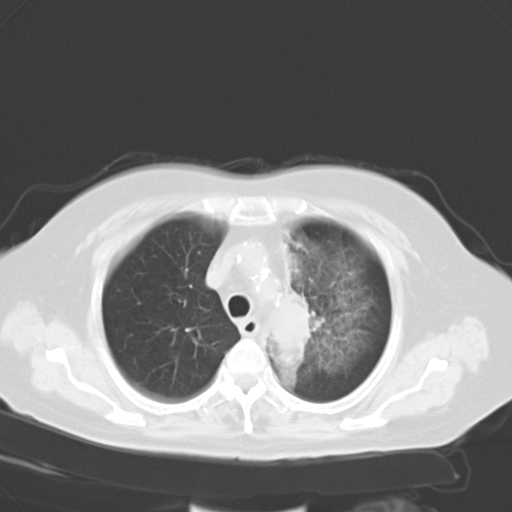
Chest CT, one axial slice; position 22 of 28 along the scan axis; 120 kVp; lung window (W 1500 / L -600 HU); 10 mm slice thickness; 512 × 512 image matrix. Patient: female, 65 years. Case-level facts recorded for this patient, not image findings: clinical TNM (as recorded): T2b N1 M0.
Structures marked on this image (rectangle marked by the reading radiologist):
- lung tumour (recorded histology: adenocarcinoma): bounding box (x1, y1, x2, y2) in pixels: (268, 295, 318, 364)